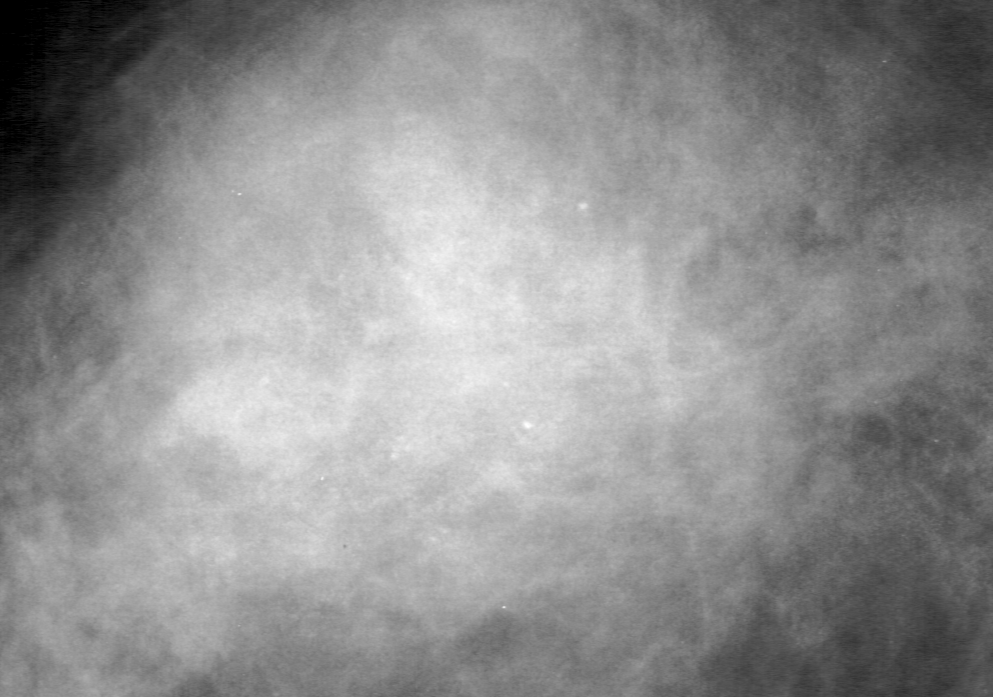
Region of interest cut from a scanned film mammogram (one marked finding); left breast; MLO view; BI-RADS breast density category 4 (scale 1–4).
Calcifications, morphology pleomorphic, distribution segmental; BI-RADS assessment category 4; pathology result (as recorded, not read from the image): malignant.